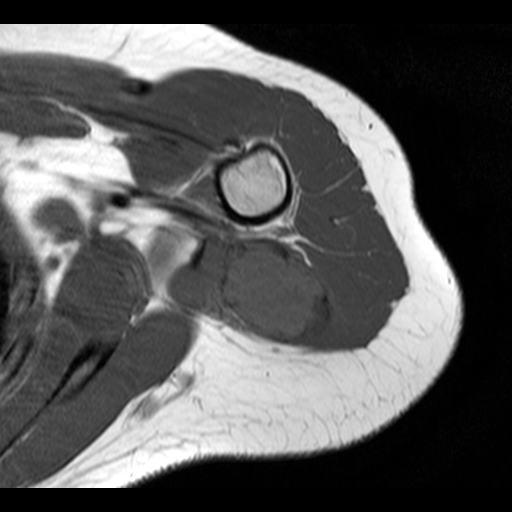
MRI of an extremity soft-tissue mass, one axial slice. Position 8 of 20 along the scan axis. 512 × 512 image matrix, field of view 150 × 150 mm. Female patient. From the clinical record (not read from this slice): histological type: malignant fibrous histiocytoma; grade: low; site of the primary tumour: left arm.
Annotated regions visible in this slice (outlined manually by an expert reader):
- gross tumour volume (mass): box from (x=218, y=234) to (x=340, y=349) px